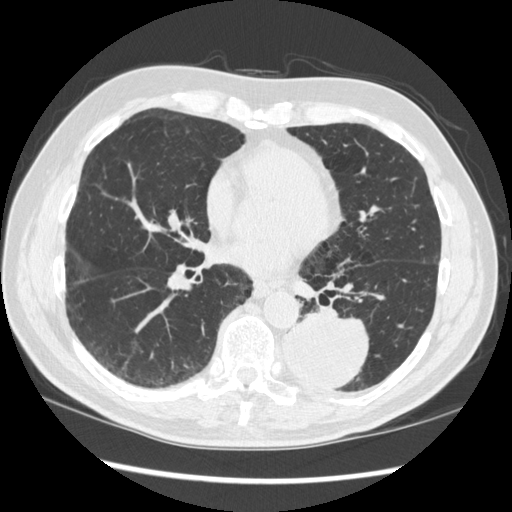
Low-dose screening chest CT, one axial slice. Reconstruction kernel STANDARD. 120 kVp. Lung window (W 1500 / L -600 HU). 1.25 mm slice thickness. 512 × 512 image matrix, field of view 360 × 360 mm.
Outlined on this slice (manually delineated by an expert):
- lesion 1 (tumor, lower lobe of left lung): bounding box <283,312,369,390> (left, top, right, bottom; pixels)